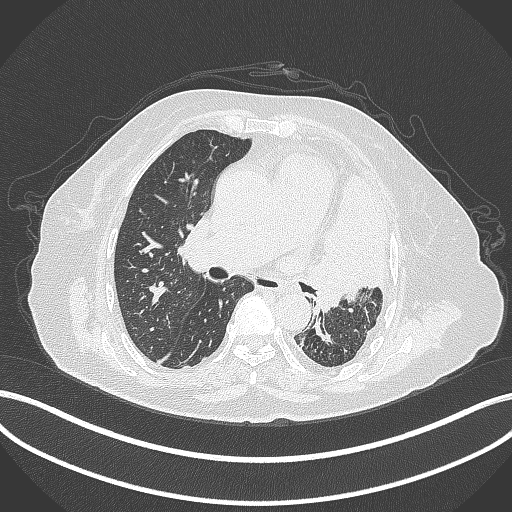
Chest CT, one axial slice; slice 214 of 399 in the series (ordered by position); reconstruction kernel B70f; lung window (W 1500 / L -600 HU); 512 × 512 image matrix, field of view 400 × 400 mm. Patient: female, 75 years. Case-level facts recorded for this patient, not image findings: clinical TNM (as recorded): T3 N3 M1.
Outlined on this slice (bounding box drawn by a radiologist):
- lung tumour (recorded histology: adenocarcinoma): bounding box <305,171,390,313> (left, top, right, bottom; pixels)